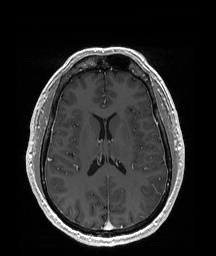
Brain MRI from a brain-tumour surgery series, one axial slice. Position 87 of 192 along the scan axis. T1-weighted post-contrast. 1 mm slice thickness. 216 × 256 image matrix, field of view 219 × 260 mm. Case-level facts recorded for this patient, not image findings: histopathology: Glioblastoma; WHO grade: 4; IDH mutation: no.
Annotated regions visible in this slice (outlined manually by an expert reader):
- tumour: bounding box (x1, y1, x2, y2) in pixels: (140, 177, 167, 211)